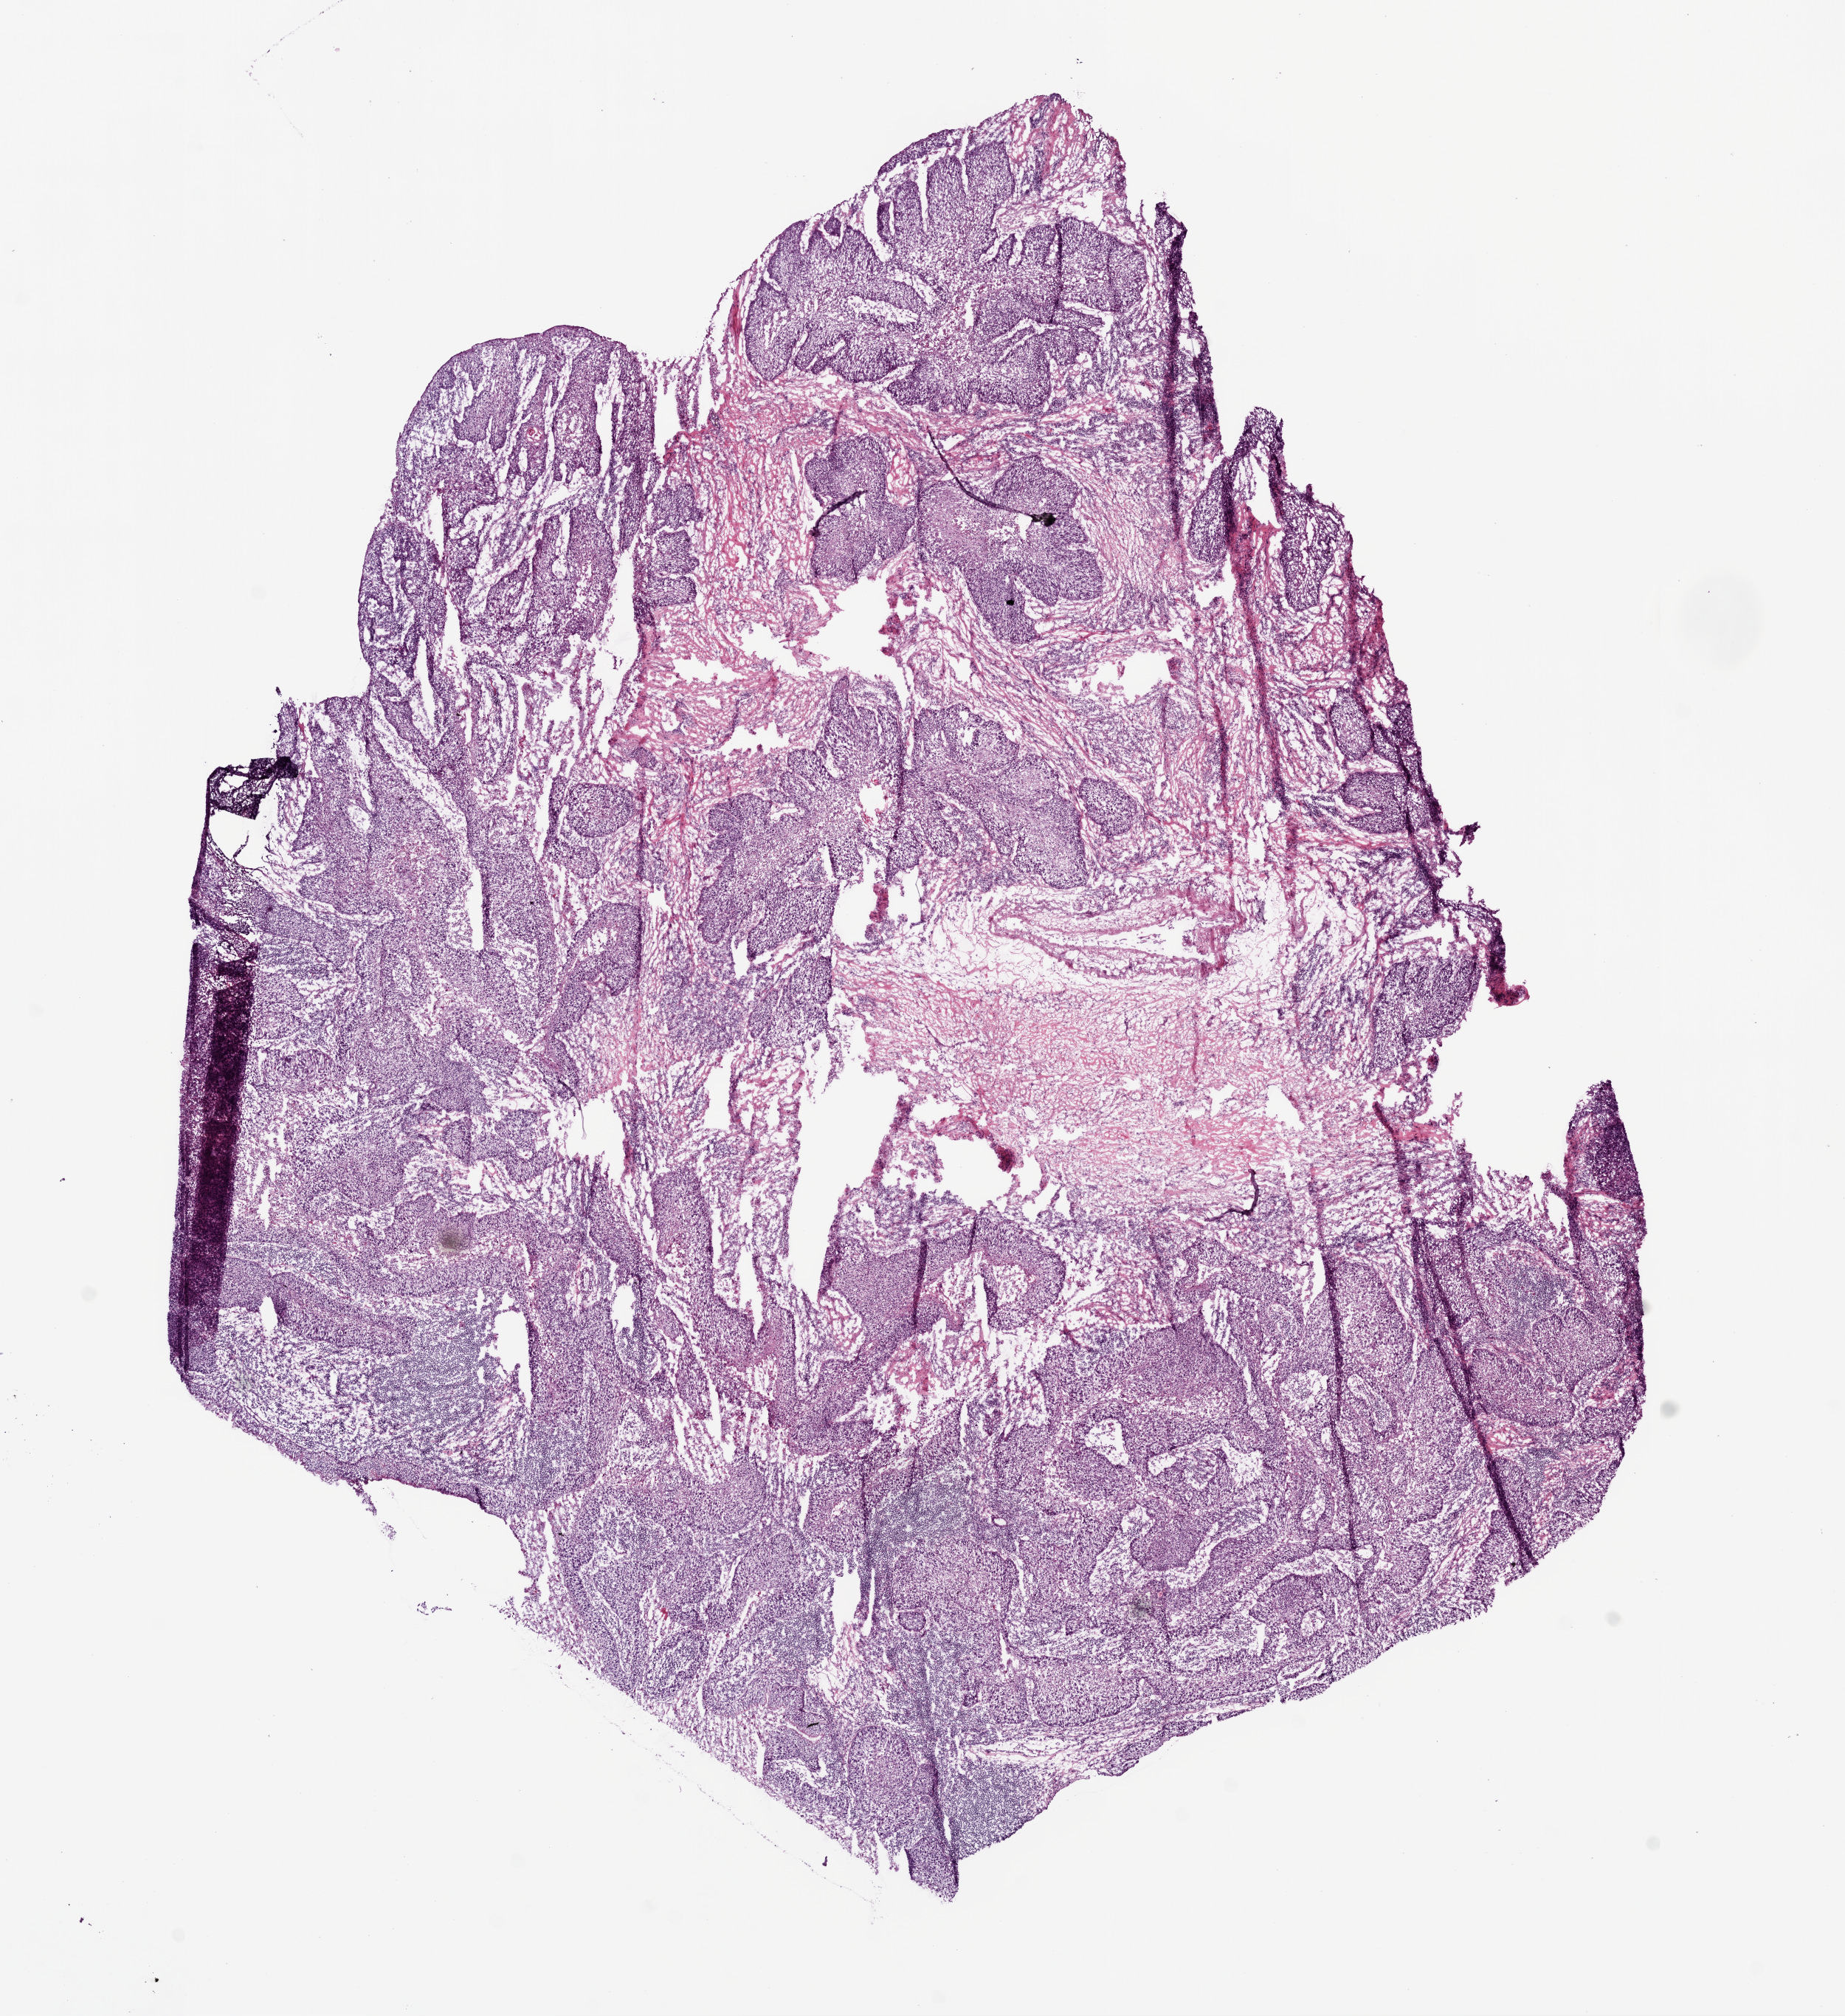
Digitized Hematoxylin and eosin (H&E) stained tissue section (whole slide), shown as a low-resolution overview of the whole scanned area (about 10.0 x 11.0 mm, slide scanned at 20x). Frozen section. Primary tumour sample from the head and neck. Male, age 71 years at initial diagnosis.
Histologic diagnosis: Squamous cell carcinoma, NOS (larynx, NOS).